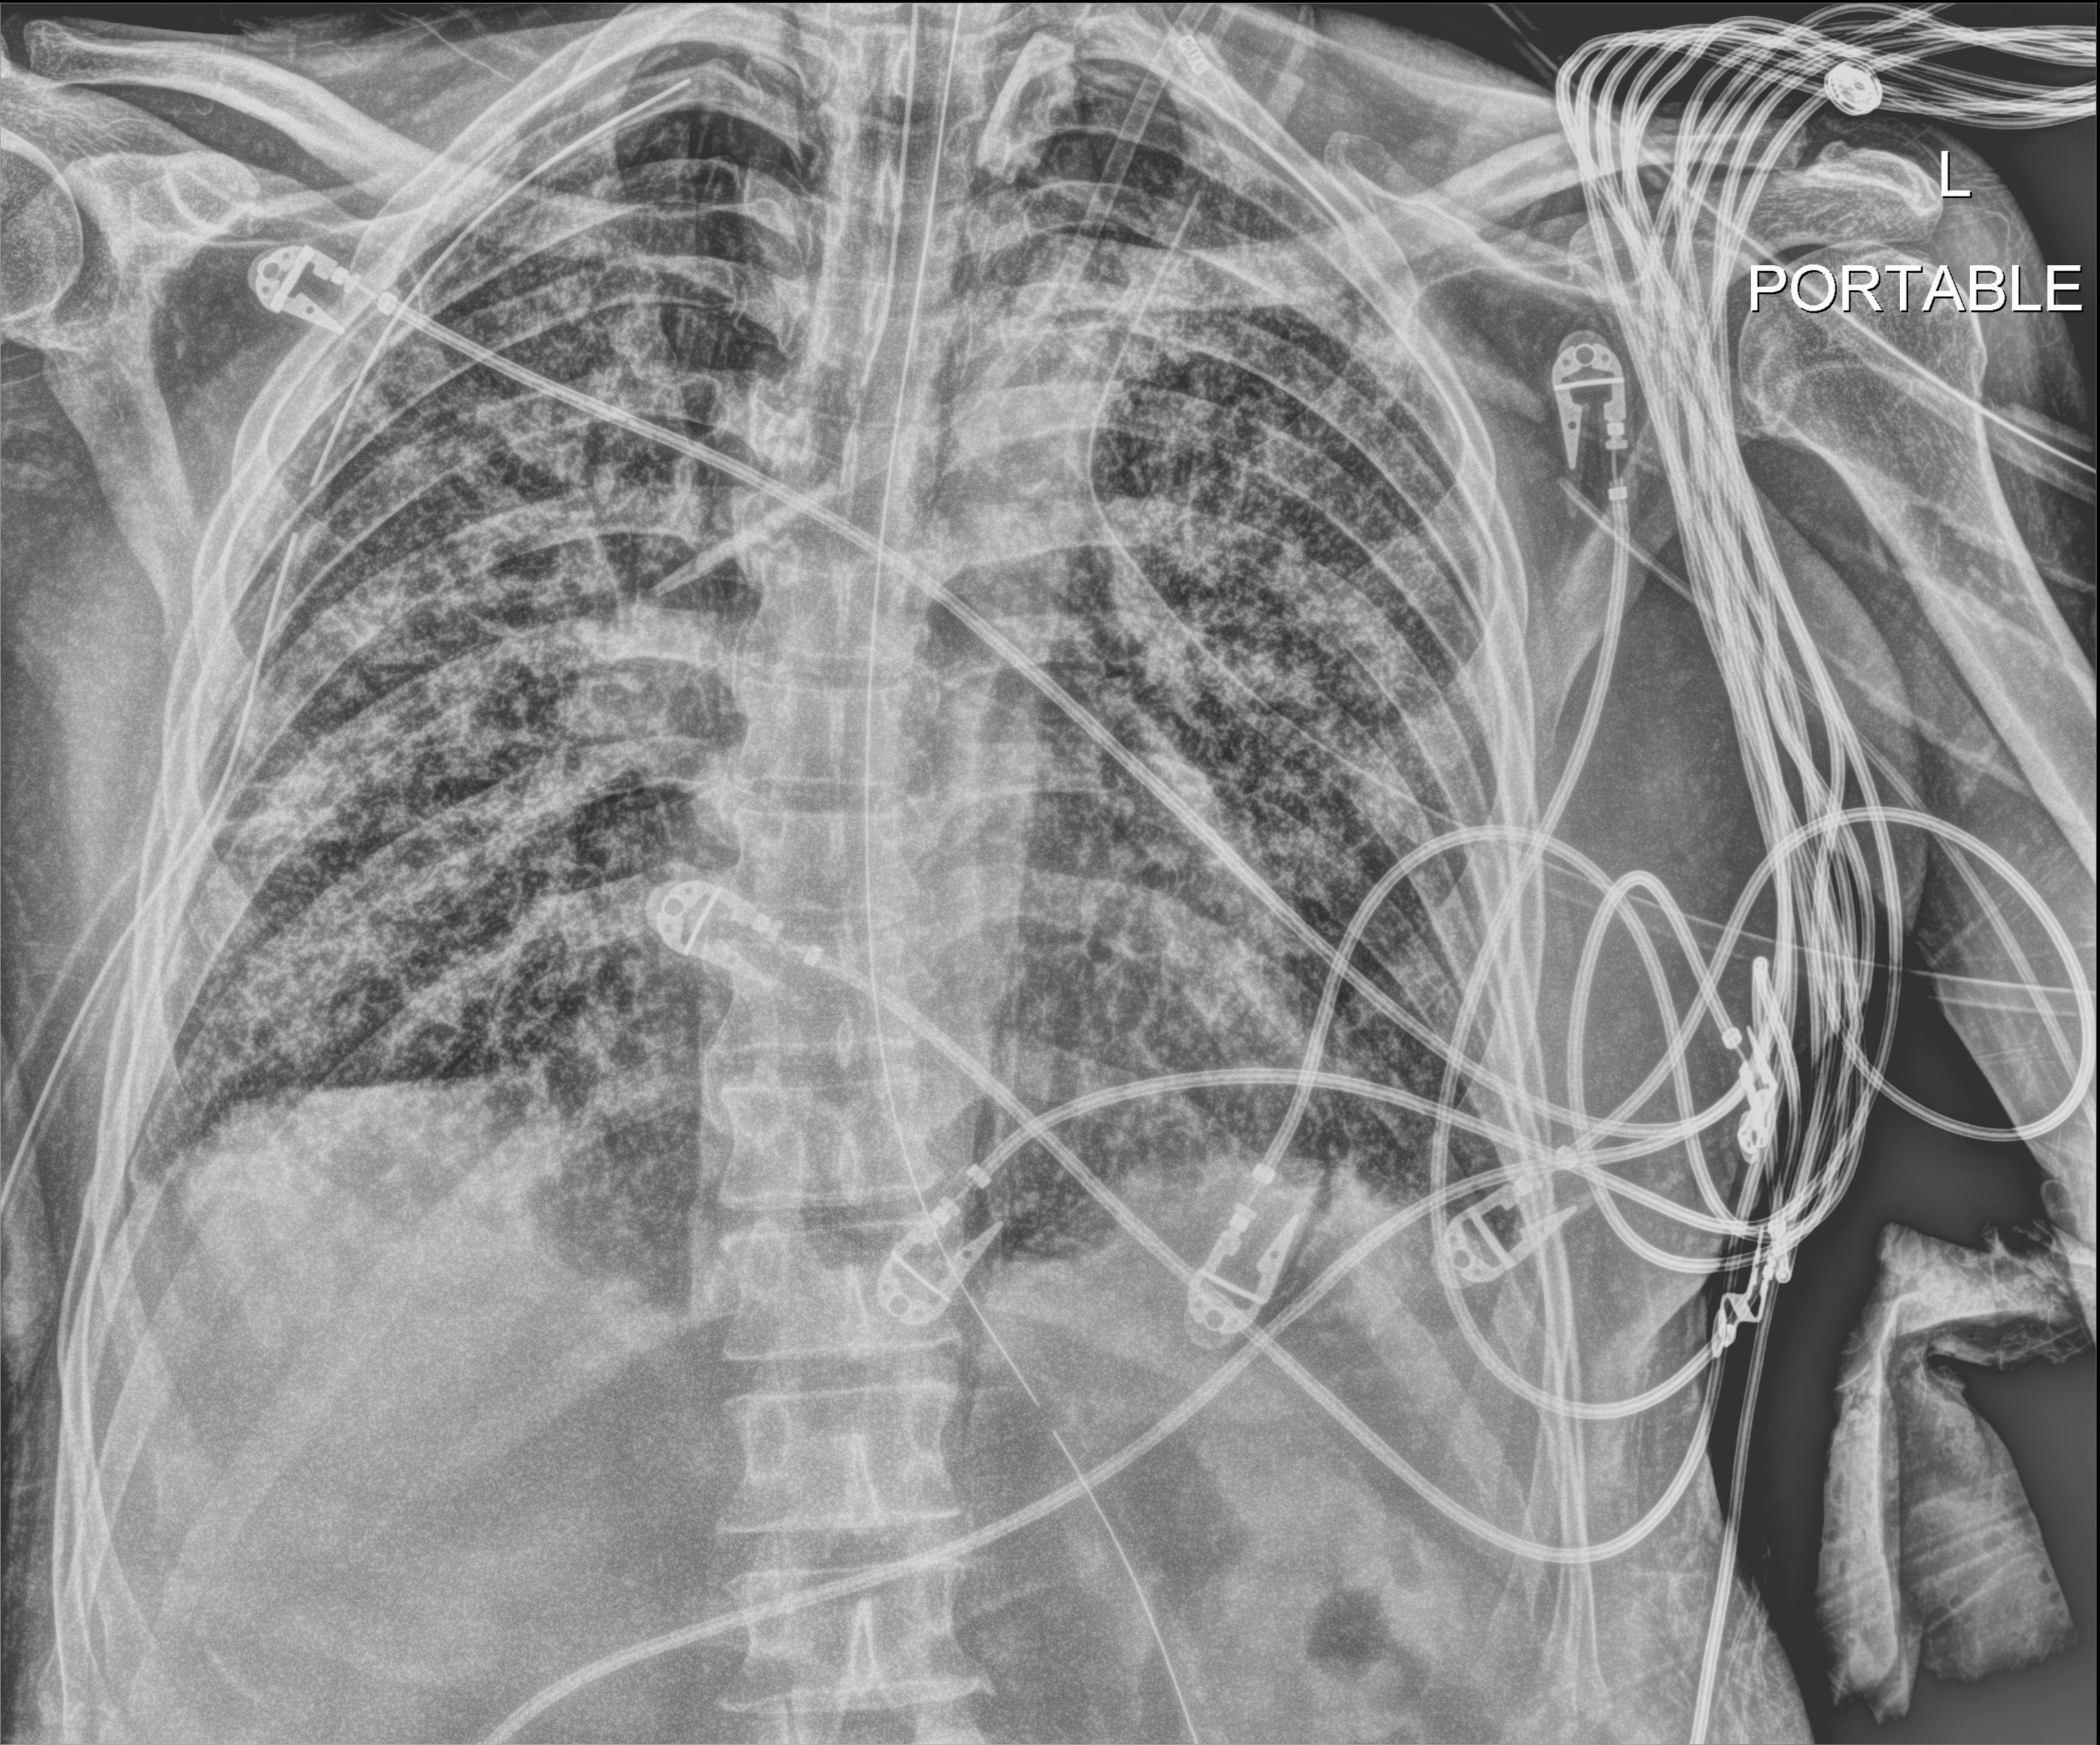
Bedside chest radiograph (digital radiography), anteroposterior (AP) projection. Male patient hospitalised with COVID-19, age 60–74 years.
Admission-level facts for this patient (not findings on this image; timing relative to this image not recorded):
- mechanically ventilated during this hospital stay: yes
- diabetes (admission record): no
- other chronic lung disease (admission record): yes